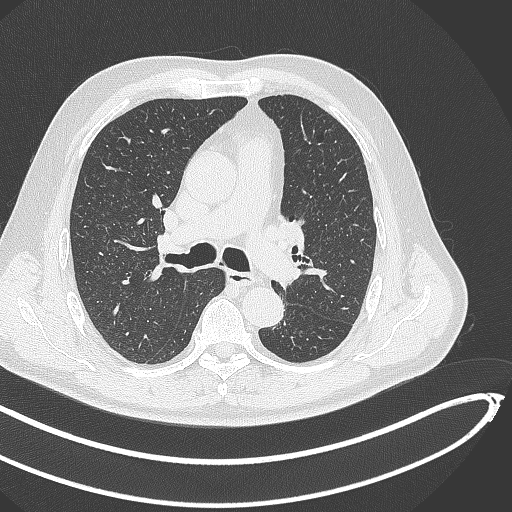
Chest CT, one axial slice; reconstruction kernel B70f; lung window (W 1500 / L -600 HU); 512 × 512 image matrix, field of view 400 × 400 mm. Male patient, age 64 years. From the clinical record (not read from this slice): clinical TNM (as recorded): T1c N0 M0; histopathological grade: G2.
Outlined on this slice (bounding box drawn by a radiologist):
- lung tumour (recorded histology: squamous cell carcinoma): bounding box [x1, y1, x2, y2] px = [276, 257, 308, 292]